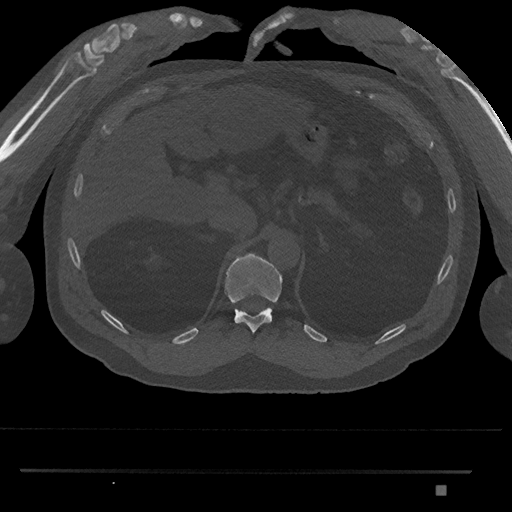
CT including the spine, one axial slice; position 940 of 1134 along the scan axis; reconstruction kernel Br40s/3; 120 kVp; bone window (W 1800 / L 400 HU); 0.5 mm slice thickness; 512 × 512 image matrix, field of view 429 × 429 mm. Patient: male, 65 years. From the clinical record (not read from this slice): primary cancer: prostate.
Structures marked on this image (semi-automatically segmented with operator editing):
- T11 vertebra: bounding box [x1, y1, x2, y2] px = [225, 253, 283, 334]